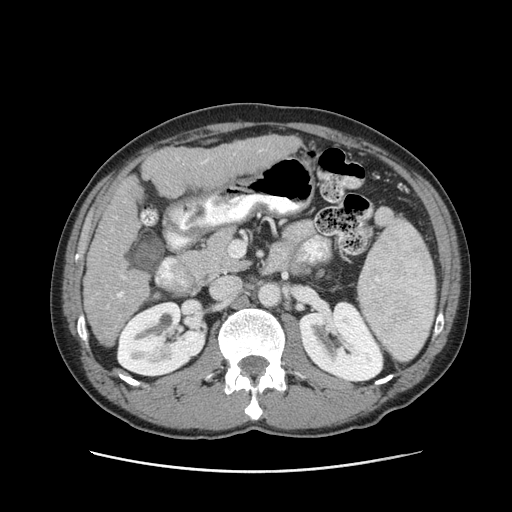
Contrast-enhanced abdominal CT (liver protocol), one axial slice. Slice 40 of 93 in the series (ordered by position). Soft-tissue window (W 400 / L 40 HU). 512 × 512 image matrix, field of view 380 × 380 mm. From the clinical record (not read from this slice): diagnosis: hepatocellular carcinoma (patient treated with transarterial chemoembolisation; whether this scan precedes or follows treatment is not stated here); TNM stage (as recorded): Stage-II; Child-Pugh class: A; tumour differentiation: moderately differentiated; tumour size: 1 cm.
Structures marked on this image (semi-automatic segmentation, software-assisted and operator-edited):
- liver parenchyma outside the tumour (the mass and vessels are separate outlines, so this box may not span the whole liver): box from (x=84, y=134) to (x=300, y=346) px
- liver vessels: (x=117, y=150)–(x=262, y=298)